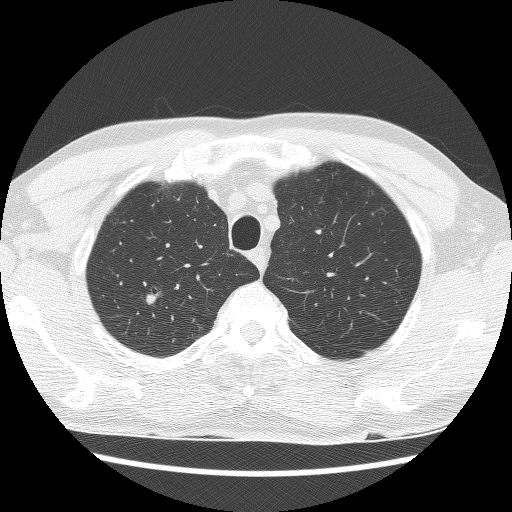
Chest CT (low-dose screening protocol), one axial image; second annual screen; lung window (W 1500 / L -600 HU); 2.5 mm slice thickness. Male, age 66 years at enrolment. Current smoker at enrolment.
Lesion marked by an expert reader, bounding box (x1, y1, x2, y2) in pixels: (137, 285, 170, 312). Reader record for this screening exam (exam-level; its link to the box is not recorded): non-calcified nodule or mass ≥4 mm, right upper lobe, 7 × 6 mm, poorly defined margins, mixed attenuation, pre-existing on the prior screen: yes; interval growth: yes. Official screen result: positive, other.